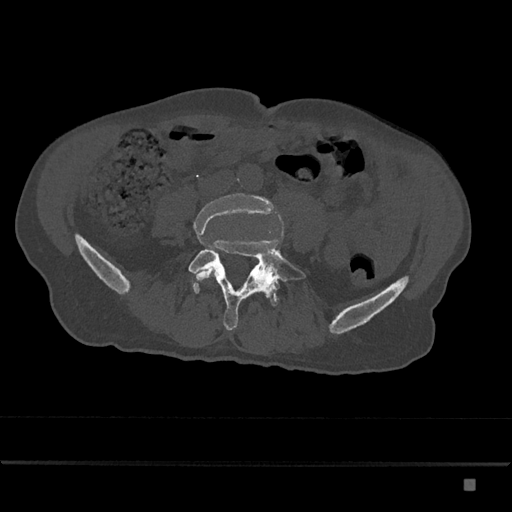
CT including the spine, one axial slice. Slice 295 of 797 in the series (ordered by position). Reconstruction kernel Br40s/3. 120 kVp. Bone window (W 1800 / L 400 HU). 0.5 mm slice thickness. 512 × 512 image matrix, field of view 390 × 390 mm. Male patient, age 72 years. Case-level facts recorded for this patient, not image findings: primary cancer: prostate.
Annotated regions visible in this slice (semi-automatic segmentation, software-assisted and operator-edited):
- L4 vertebra: bounding box <193,193,275,280> (left, top, right, bottom; pixels)
- L5 vertebra: <188,212,306,330>